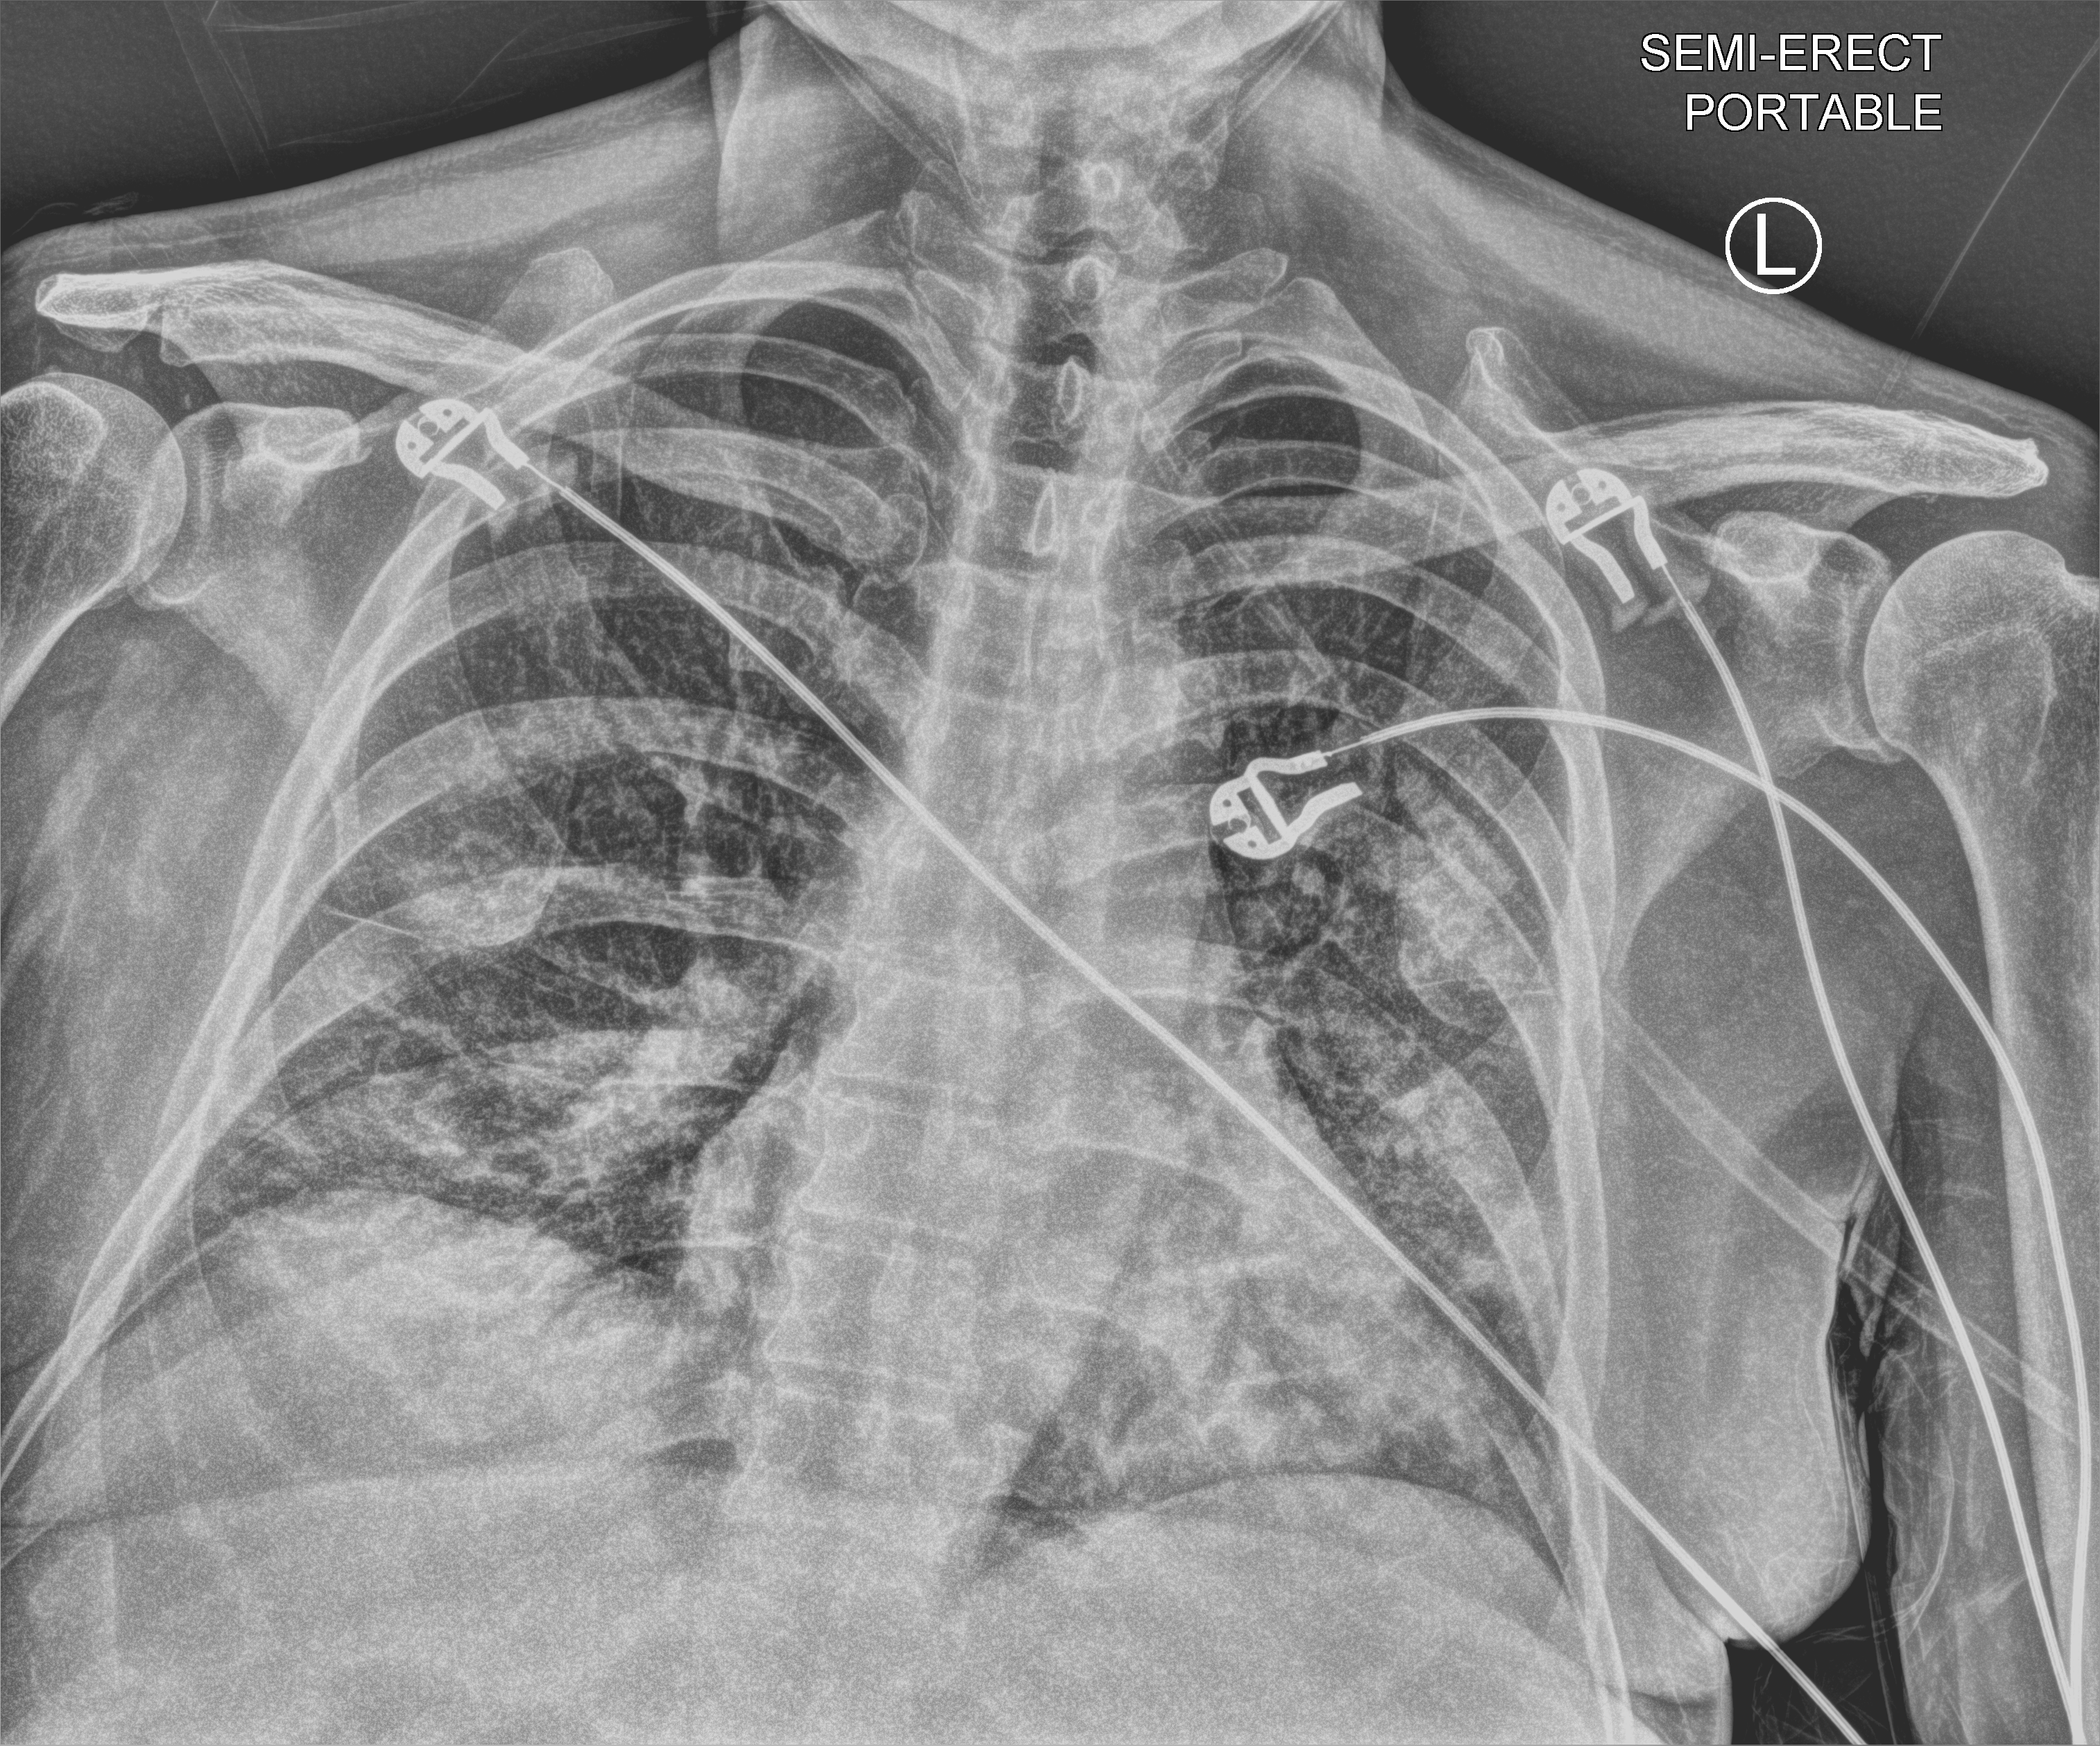
Portable chest radiograph, anteroposterior (AP) projection. Patient hospitalised with COVID-19; male, aged 60–74 years.
From the hospital-stay record, not from the radiograph (when in the stay this image was taken is not recorded): mechanically ventilated during this hospital stay: no.